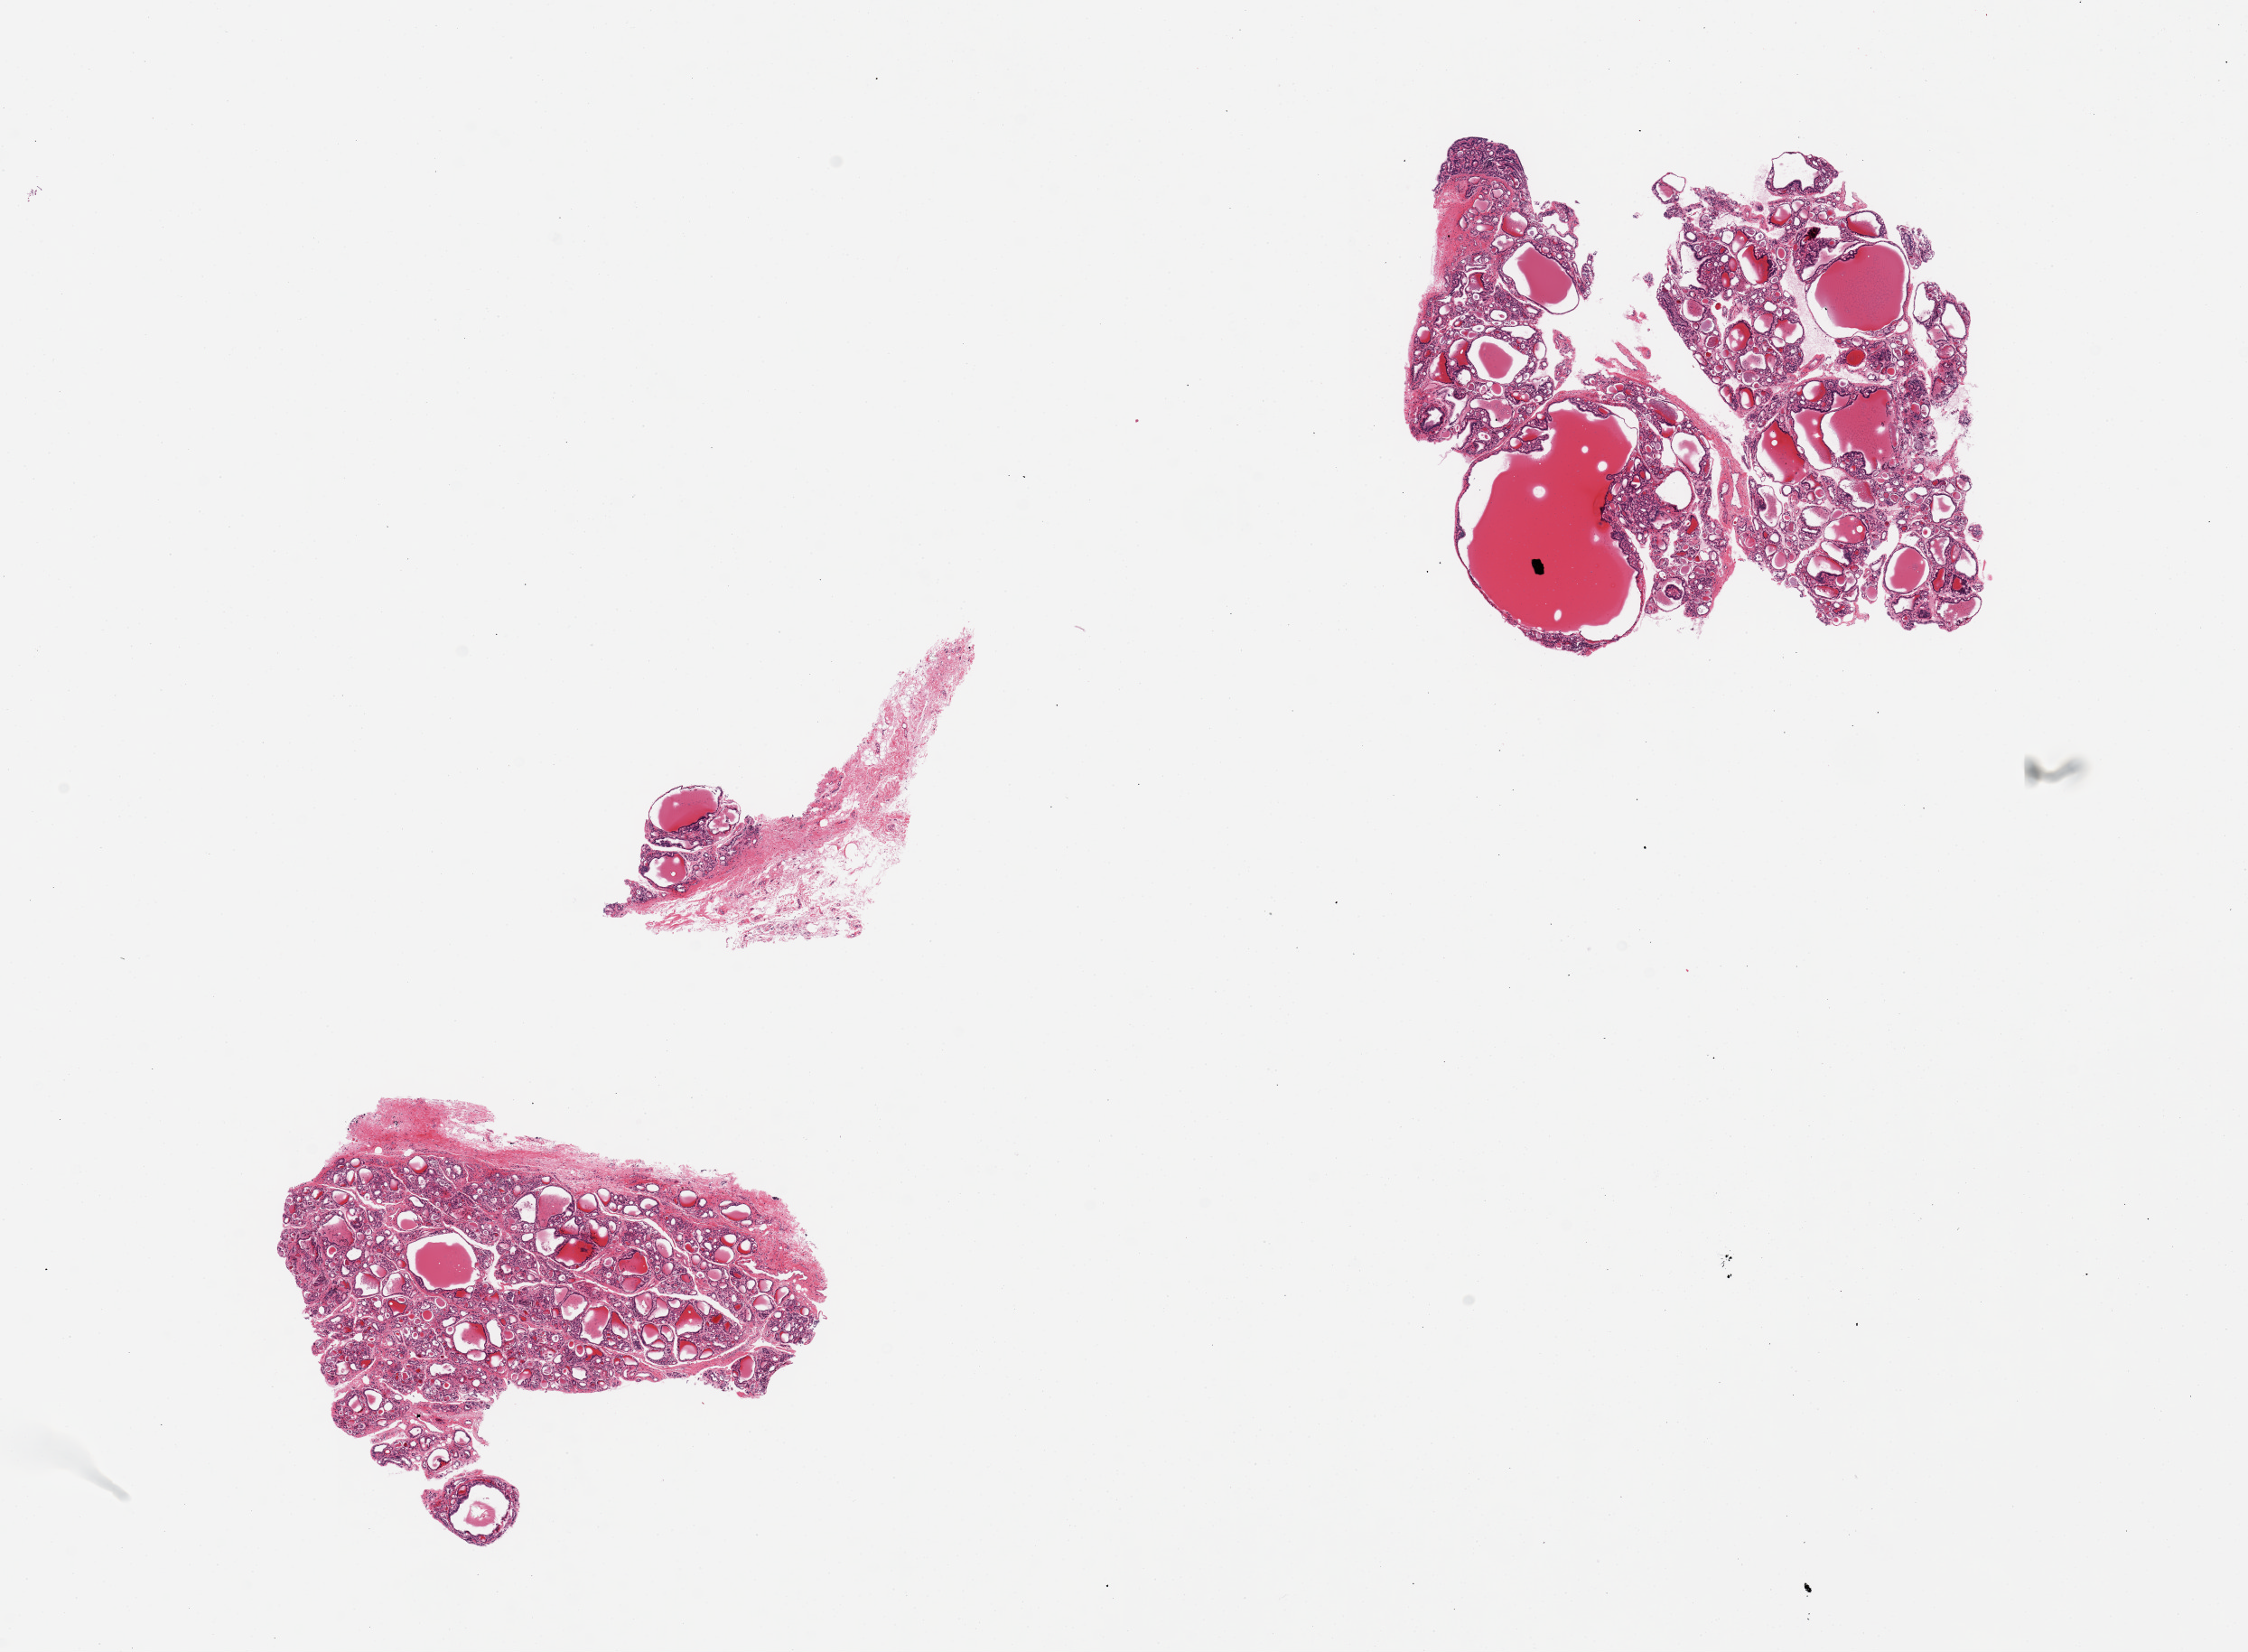
Whole-slide image, hematoxylin and eosin (H&E) stain — a low-resolution overview of the entire scanned area, about 19.7 x 14.5 mm (slide scanned at 20x). PAXgene-fixed, paraffin-embedded tissue. Section of thyroid (target tissue). Donor tissue sample. Donor sex: male.
Review note (as recorded): 3 small, irregular, fragmented pieces; nodular; smallest piece is largely fat and fibrous stroma.